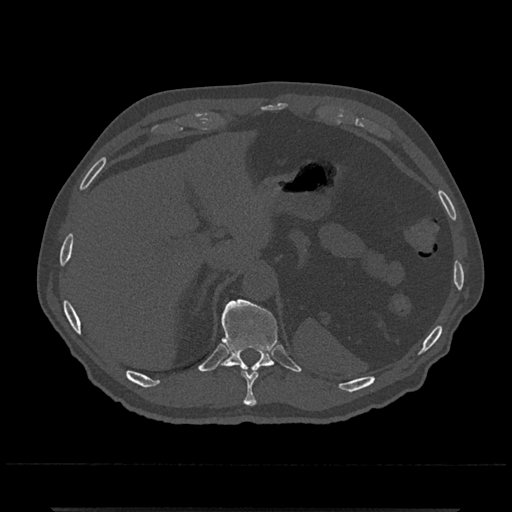
CT including the spine, one axial slice; slice 514 of 797 in the series (ordered by position); reconstruction kernel Br40s/3; bone window (W 1800 / L 400 HU); 0.5 mm slice thickness; 512 × 512 image matrix. Patient: male, 67 years. From the clinical record (not read from this slice): primary cancer: prostate.
Outlined on this slice (semi-automatic segmentation, software-assisted and operator-edited):
- T10 vertebra: bounding box <242,370,258,406> (left, top, right, bottom; pixels)
- T11 vertebra: <216,299,278,372>